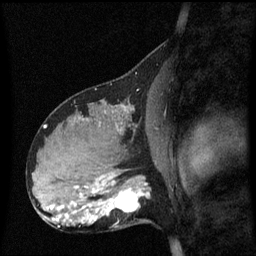
Breast MRI (dynamic contrast-enhanced), one sagittal slice; position 33 of 60 along the scan axis; dynamic contrast-enhanced series, image 2 of 3 at this slice position (ordered by acquisition); 1.5 T; TE 4.2 ms, TR 8.4 ms; 256 × 256 image matrix, field of view 210 × 210 mm. Patient: female, 31 years. From the clinical record (not read from this slice): setting: breast cancer imaged before/during neoadjuvant chemotherapy; receptor status: HR-positive, HER2-negative.
Structures marked on this image (semi-automatically segmented with operator editing):
- analysis volume of interest (the breast-tissue region the enhancement analysis was run in; not a lesion): bounding box [x1, y1, x2, y2] px = [98, 175, 153, 228]
- tumour enhancement mask (voxels above the 70 % enhancement threshold inside the analysis volume of interest): [100, 177, 150, 216]